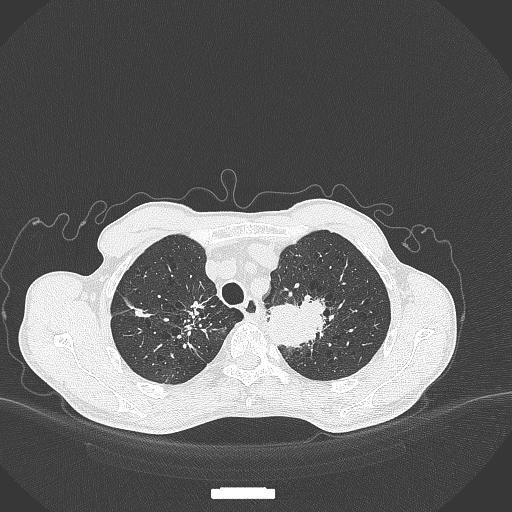
Chest CT, one axial slice. Slice 350 of 386 in the series (ordered by position). 120 kVp. Lung window (W 1500 / L -600 HU). 512 × 512 image matrix, field of view 400 × 400 mm. Patient: male, 65 years. From the clinical record (not read from this slice): clinical TNM (as recorded): T2b N0 M0; histopathological grade: G2.
Outlined on this slice (rectangle marked by the reading radiologist):
- lung tumour (recorded histology: adenocarcinoma): bounding box [x1, y1, x2, y2] px = [261, 290, 330, 349]